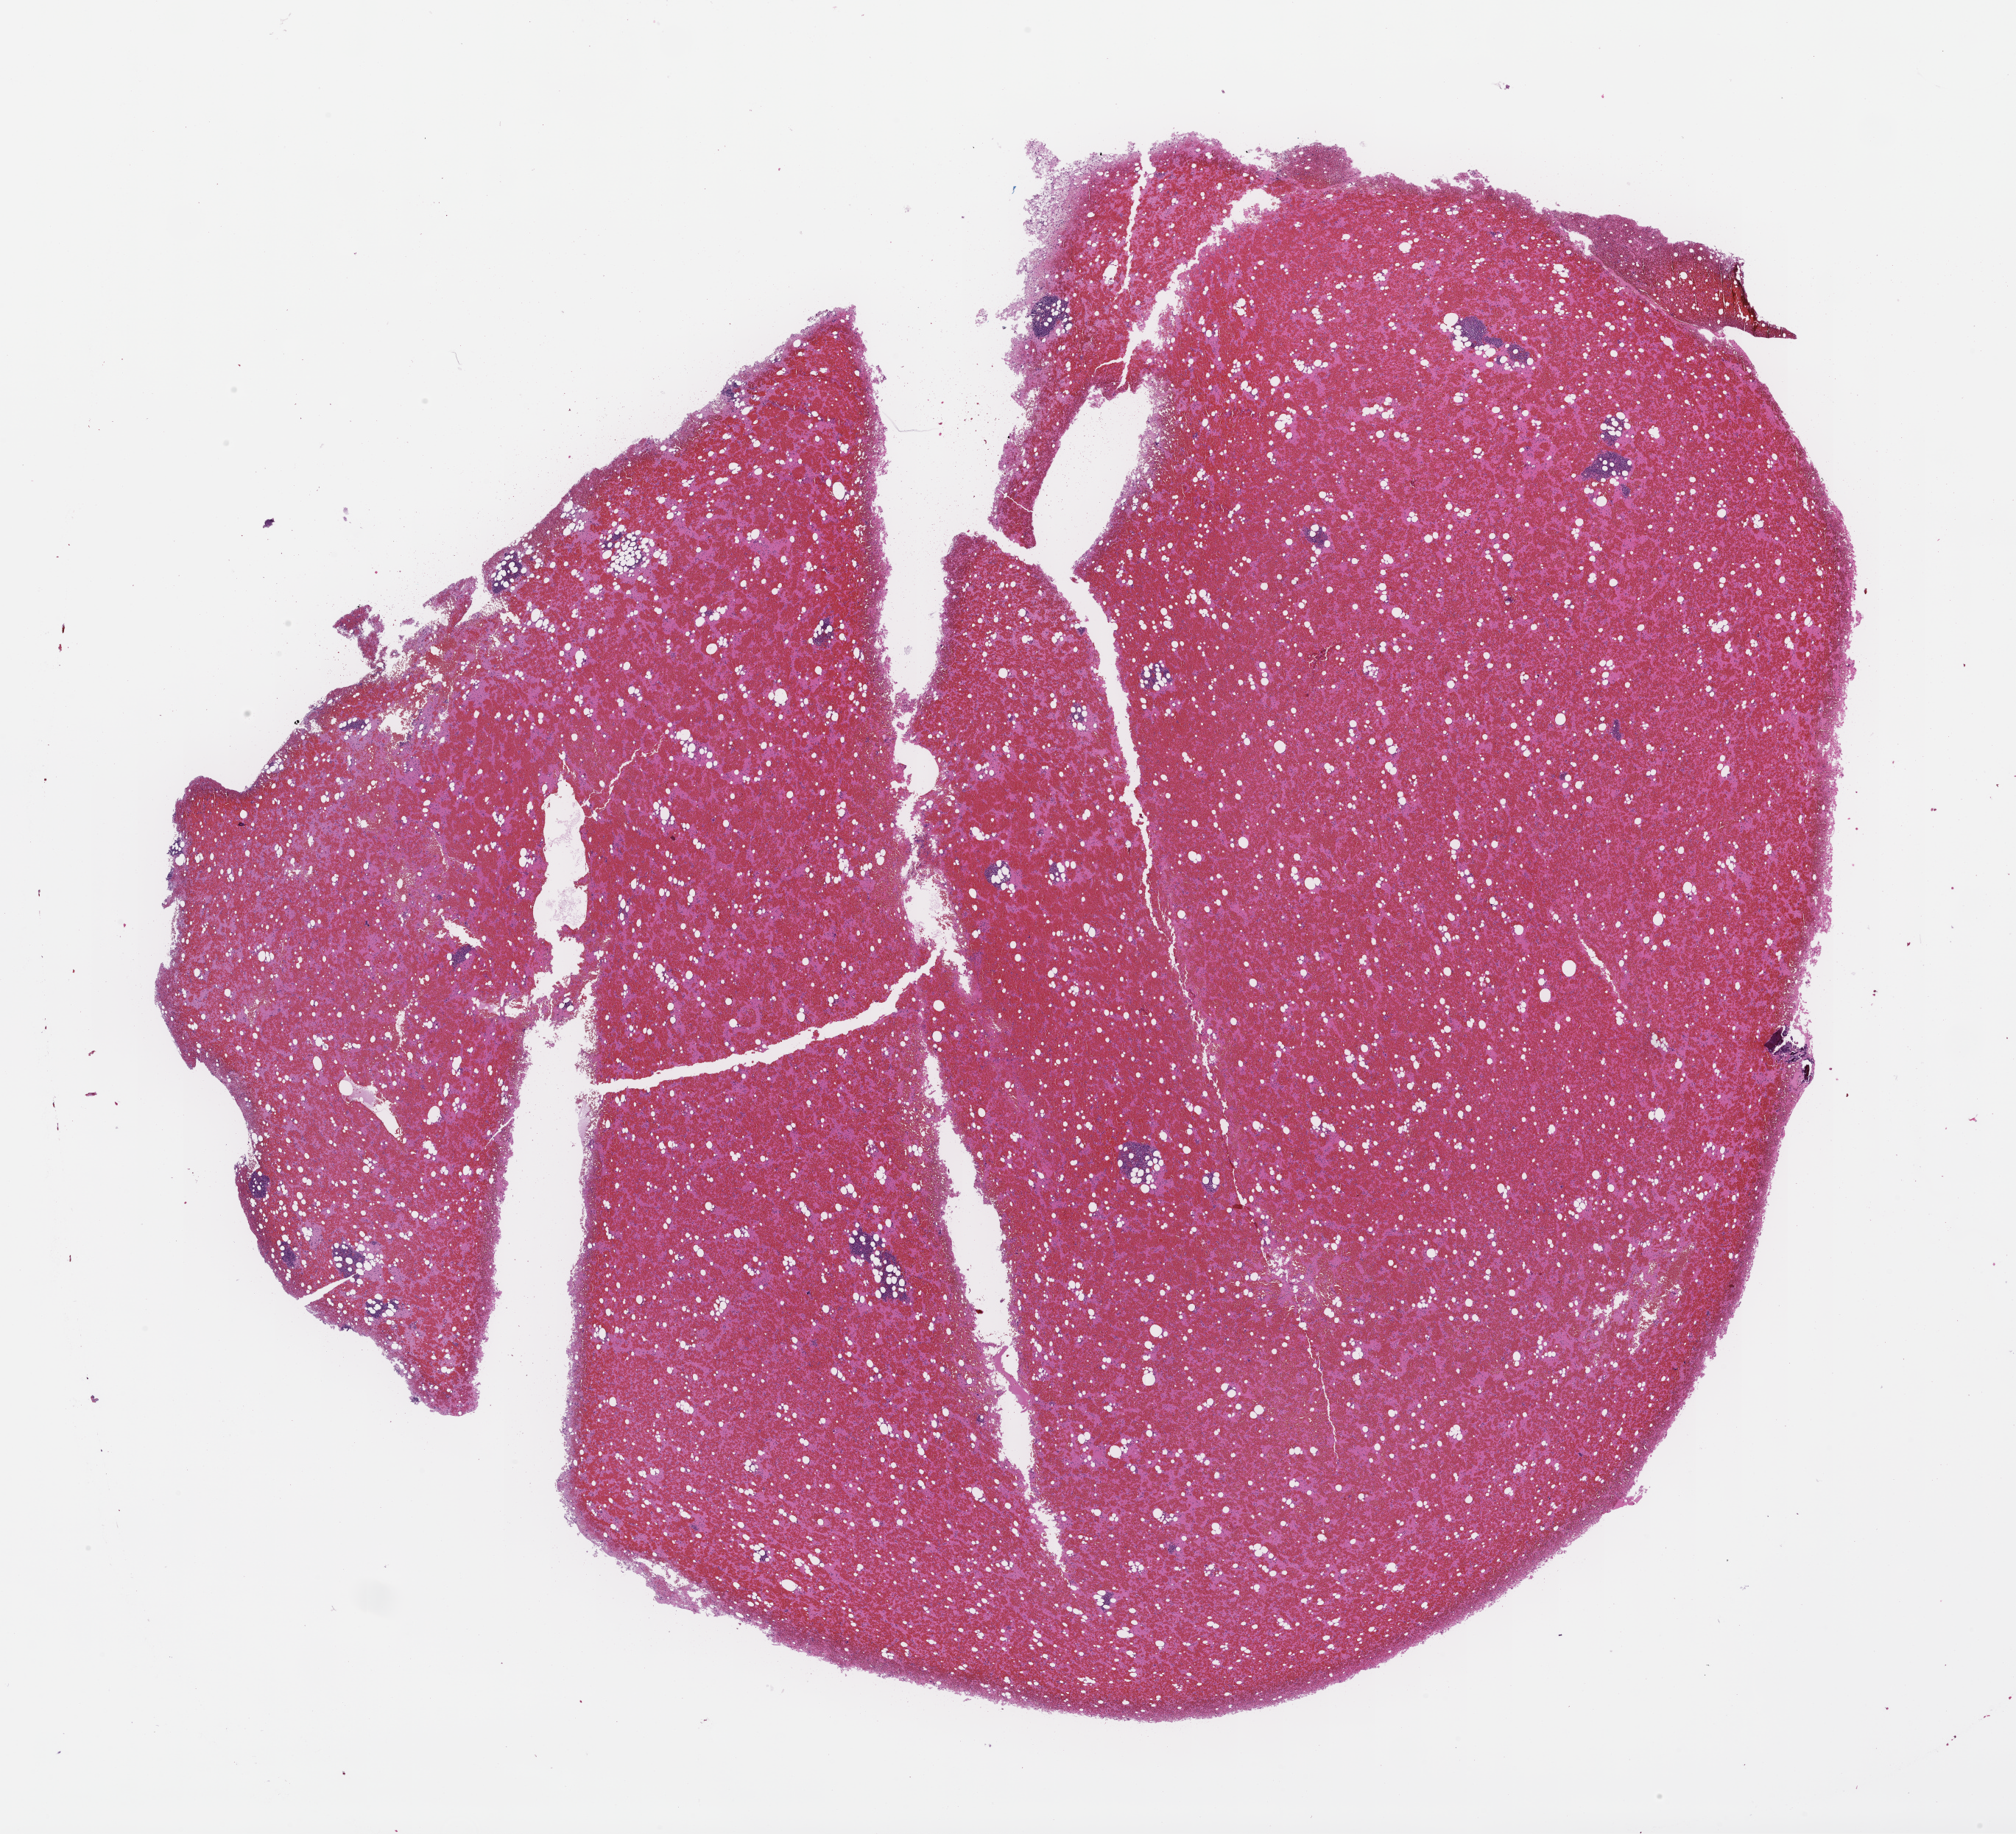
Whole-slide image, hematoxylin and eosin (H&E) stain — whole scanned area (about 22.1 x 20.1 mm) shown as a low-resolution overview. Formalin-fixed, paraffin-embedded (FFPE) tissue. Tissue site: bone marrow. Female patient.
This section: primary tumor. Diagnosis: Plasma Cell Myeloma.